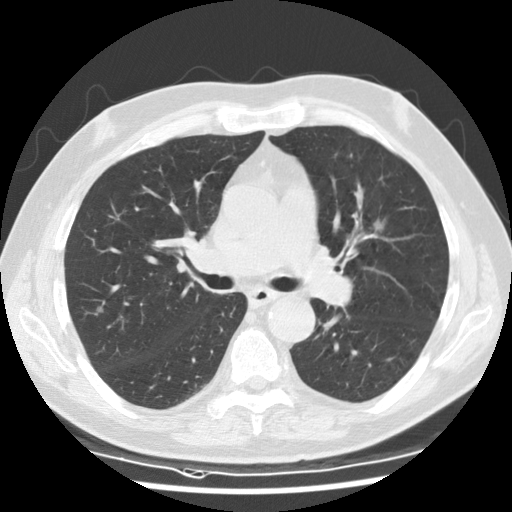
Low-dose screening chest CT, one axial slice. Position 75 of 135 along the scan axis. Reconstruction kernel STANDARD. Lung window (W 1500 / L -600 HU). 2.5 mm slice thickness. 512 × 512 image matrix, field of view 340 × 340 mm.
Annotated regions visible in this slice (expert manual segmentation):
- lesion 1 (tumor, upper lobe of left lung): box from (x=374, y=221) to (x=383, y=230) px